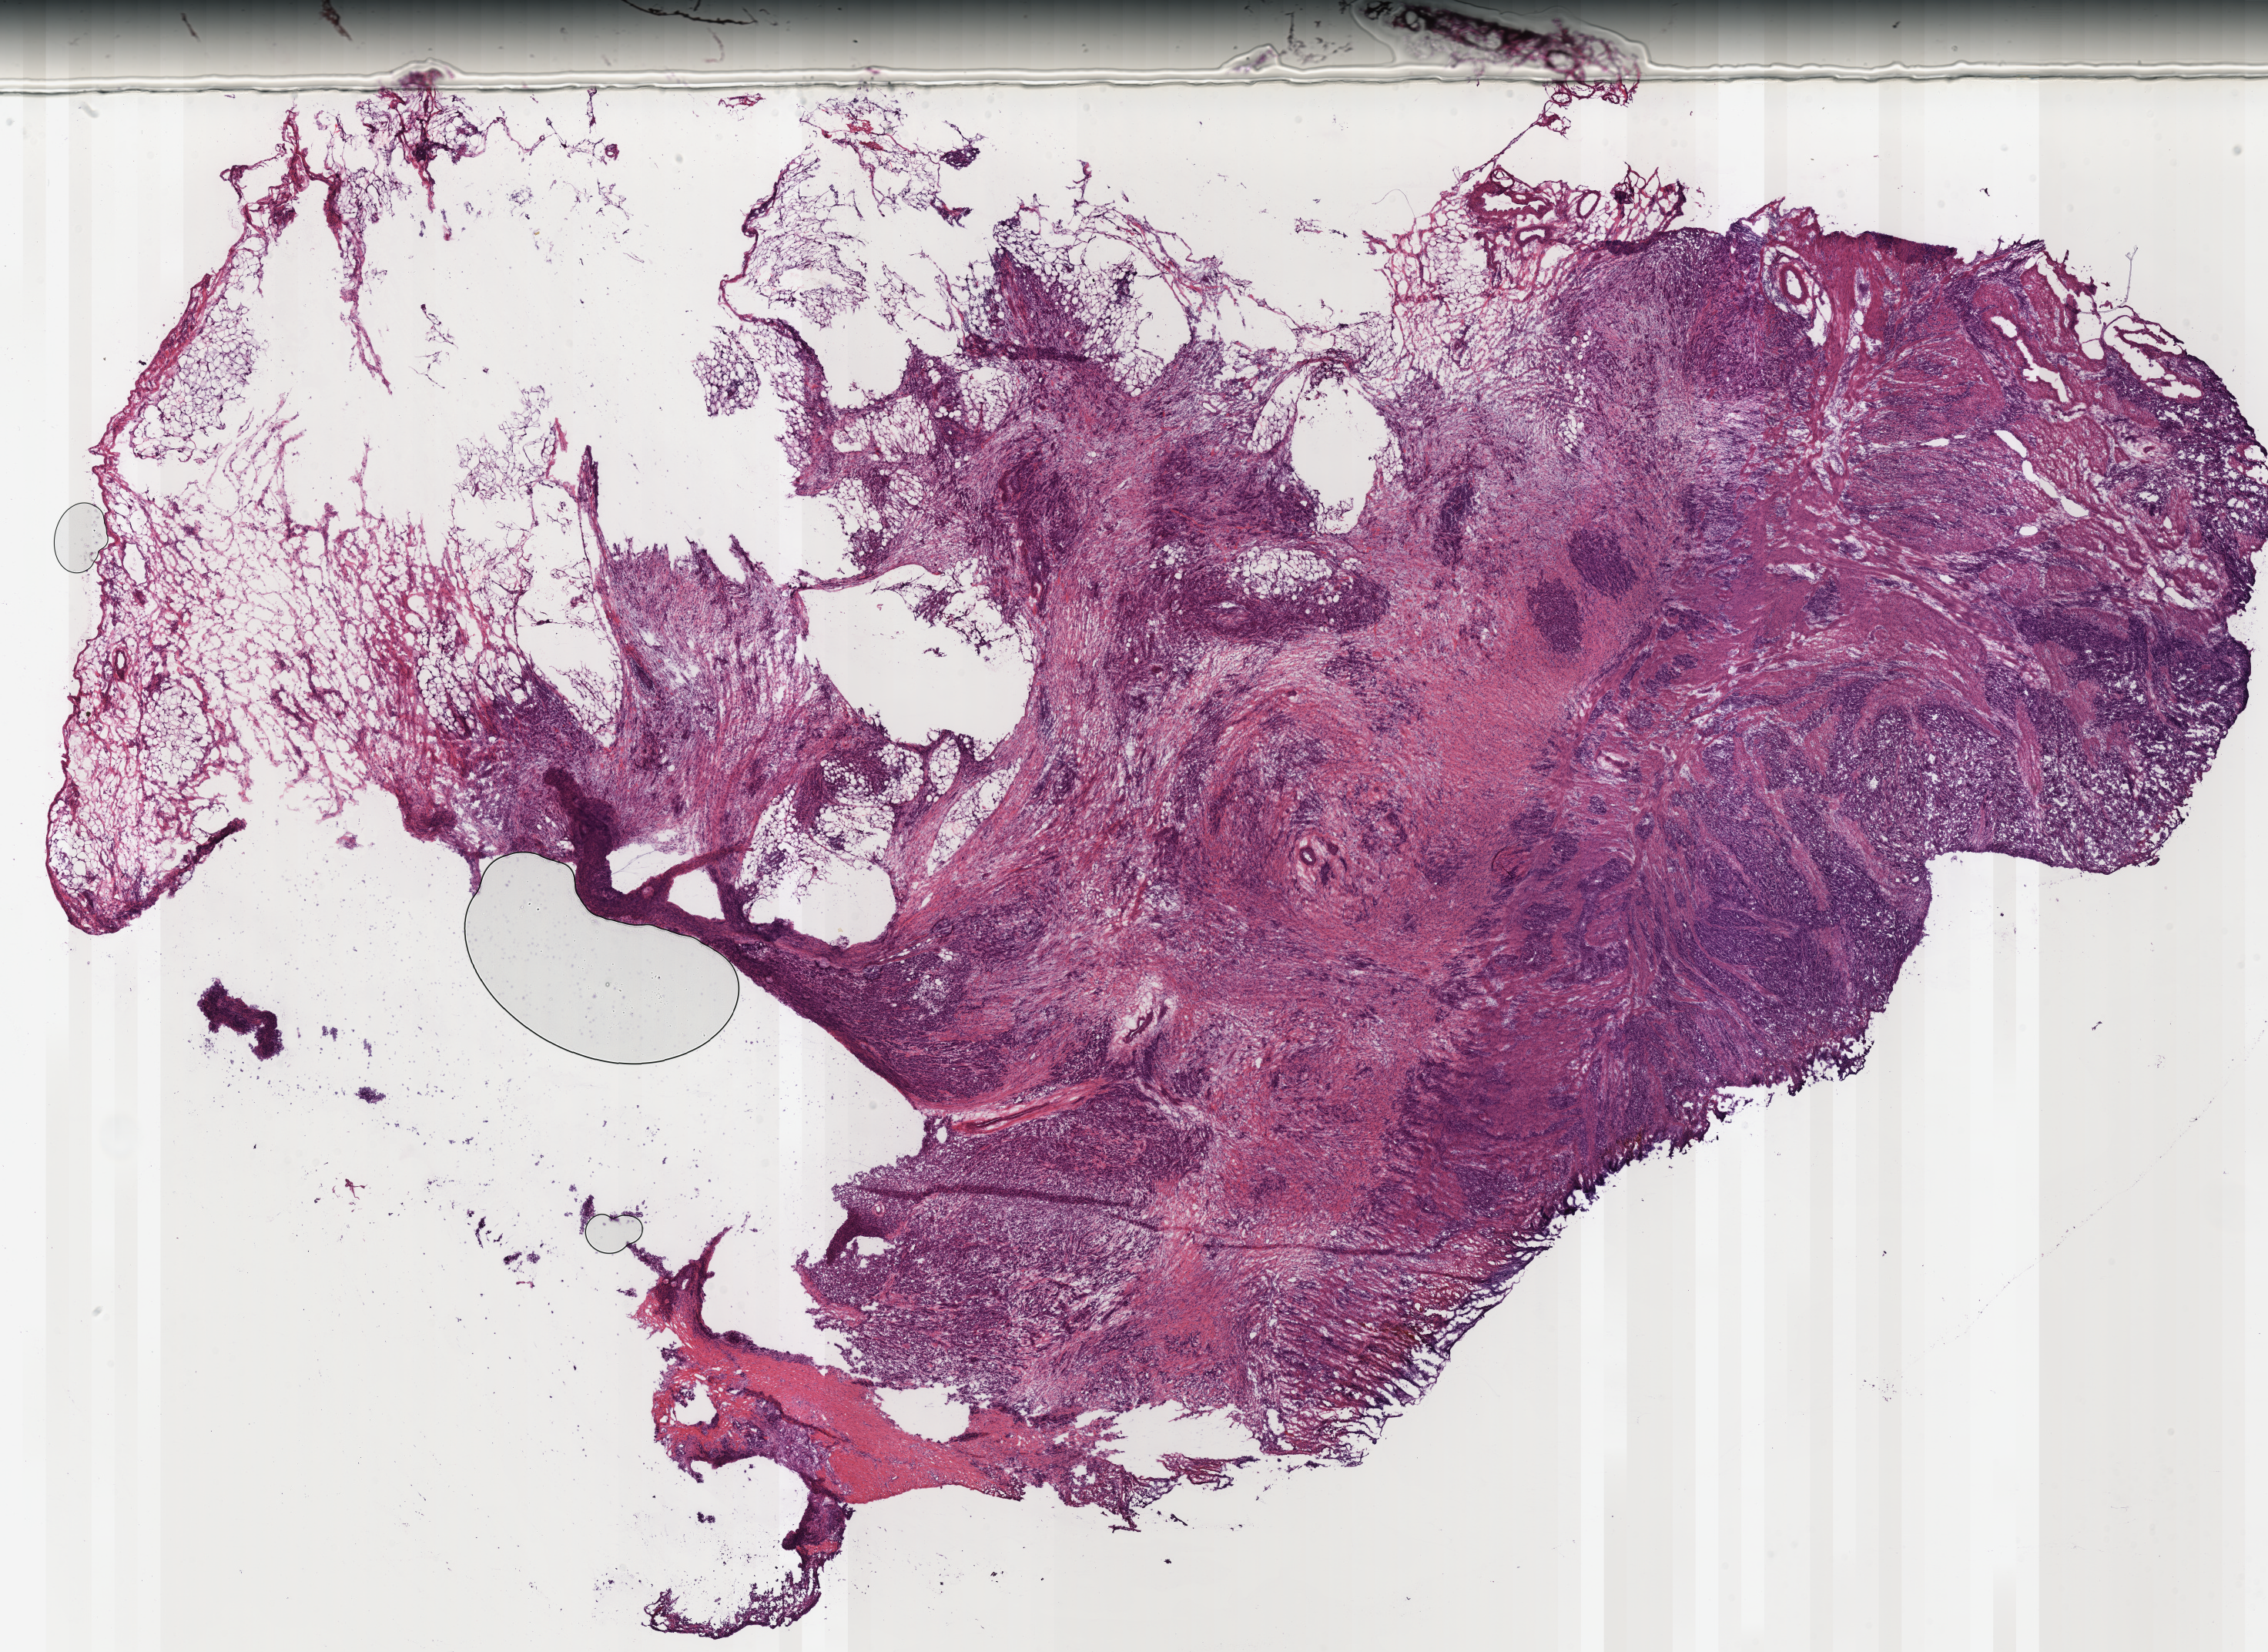
Whole-slide histology image, Hematoxylin and eosin (H&E) stained — whole scanned area (about 23.2 x 16.9 mm) shown as a low-resolution overview, frozen section from the bottom of the tissue portion, stomach, primary tumour sample. Patient: female, age at initial diagnosis 74 years. Histologic grade: G3 (poorly differentiated). Slide review estimates, as recorded: tumour cells 68%, tumour nuclei 61%, normal cells 22%, stromal cells 10%, necrosis 0%. Inflammatory infiltration, as recorded: lymphocyte infiltration 25%, monocyte infiltration 0%, neutrophil infiltration 0%.
AJCC pathologic stage: IIIB (7th edition). Diagnosis: Adenocarcinoma, NOS (gastric antrum). Lymph nodes positive (case pathology): 8 of 15 examined.